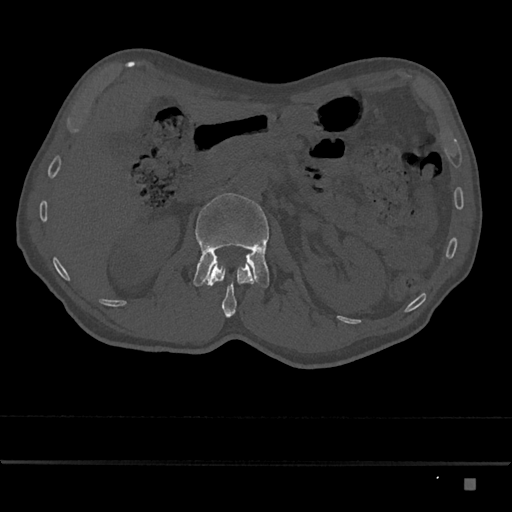
CT including the spine, one axial slice. Slice 505 of 797 in the series (ordered by position). Reconstruction kernel Br40s/3. 120 kVp. Bone window (W 1800 / L 400 HU). 512 × 512 image matrix. Male patient, age 72 years. Case-level facts recorded for this patient, not image findings: primary cancer: prostate.
Annotated regions visible in this slice (semi-automatic segmentation, software-assisted and operator-edited):
- L1 vertebra: box from (x=206, y=262) to (x=256, y=318) px
- L2 vertebra: (x=193, y=193)–(x=270, y=288)